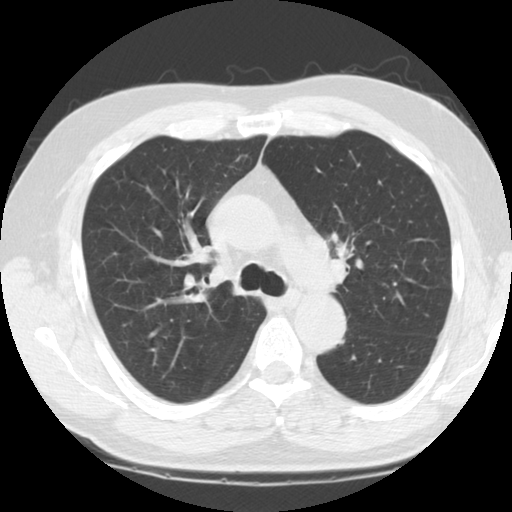
Low-dose screening chest CT, one axial slice; slice 85 of 124 in the series (ordered by position); lung window (W 1500 / L -600 HU); 2.5 mm slice thickness; 512 × 512 image matrix, field of view 340 × 340 mm.
Structures marked on this image (outlined manually by an expert reader):
- lesion 1 (tumor, upper lobe of left lung): box from (x=336, y=241) to (x=354, y=261) px